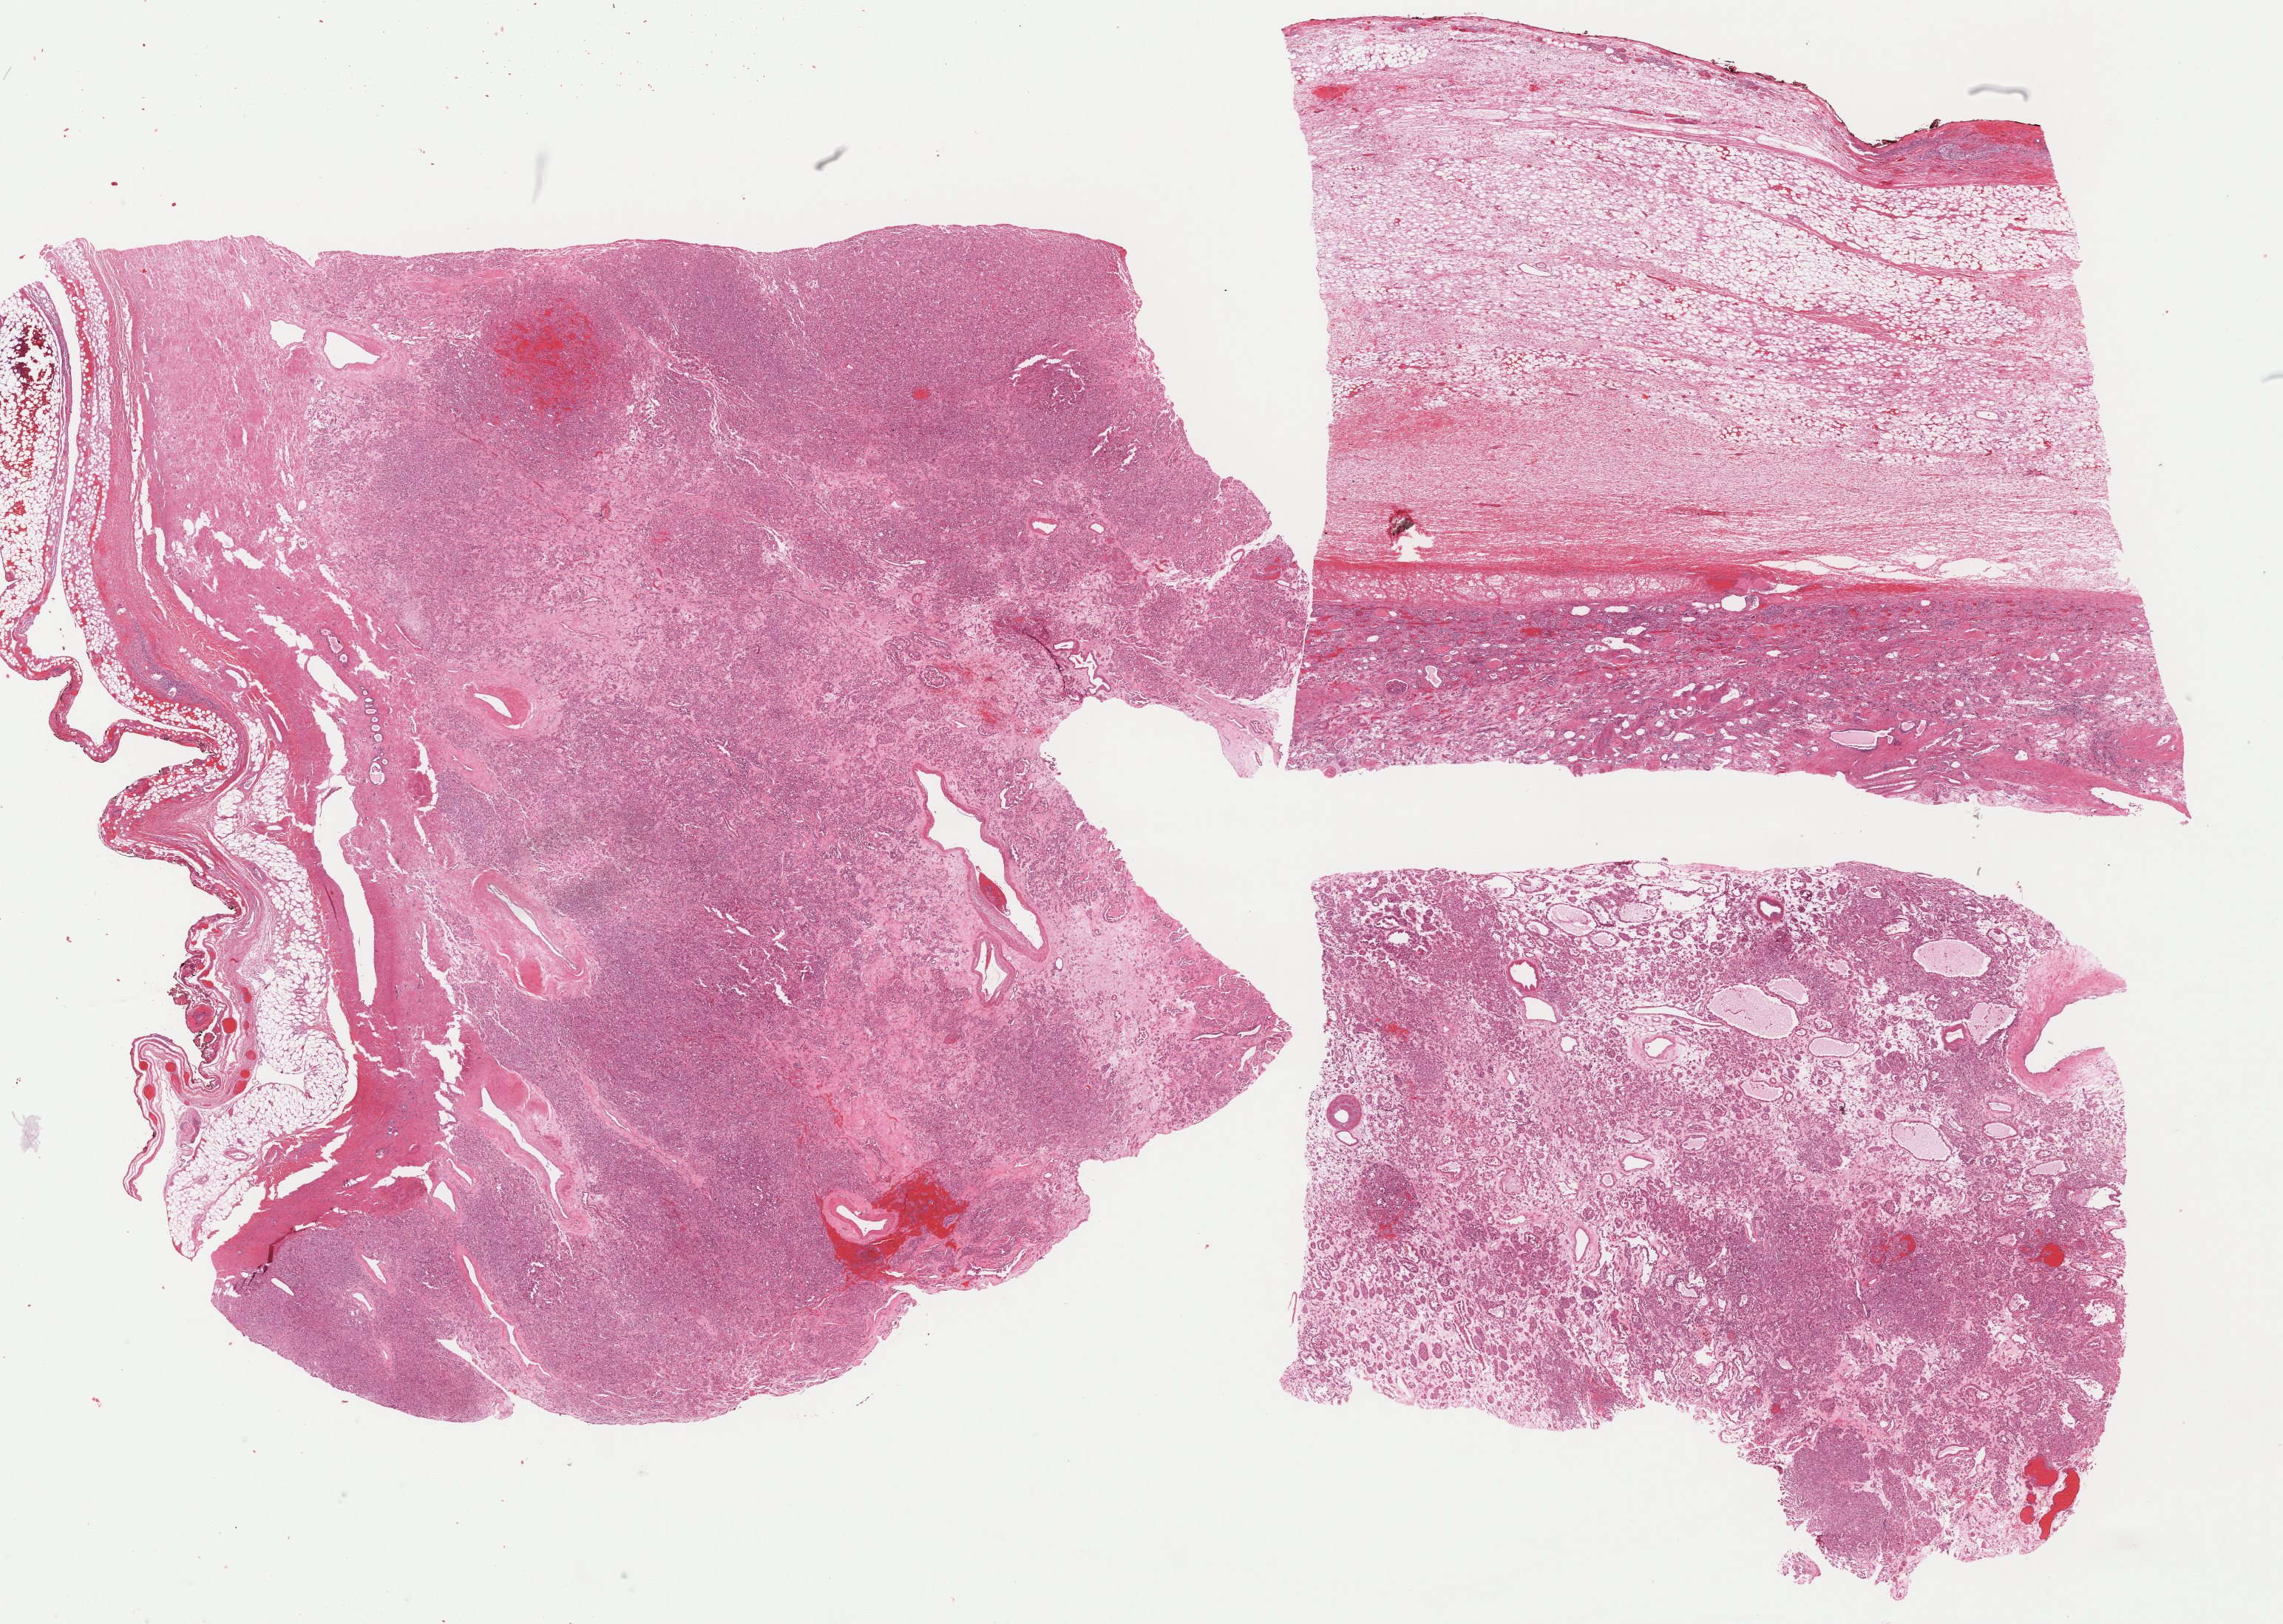
Whole-slide histology image, H&E-stained — a low-resolution overview of the entire scanned area, about 24.9 x 17.7 mm; formalin-fixed paraffin-embedded (FFPE) diagnostic section; primary tumour sample from the kidney. Male, age 54 years at initial diagnosis.
* TNM: T4 N1
* AJCC pathologic stage: IV
* lymph nodes positive (case pathology): 1 of 4 examined
* histologic diagnosis: Renal cell carcinoma, chromophobe type